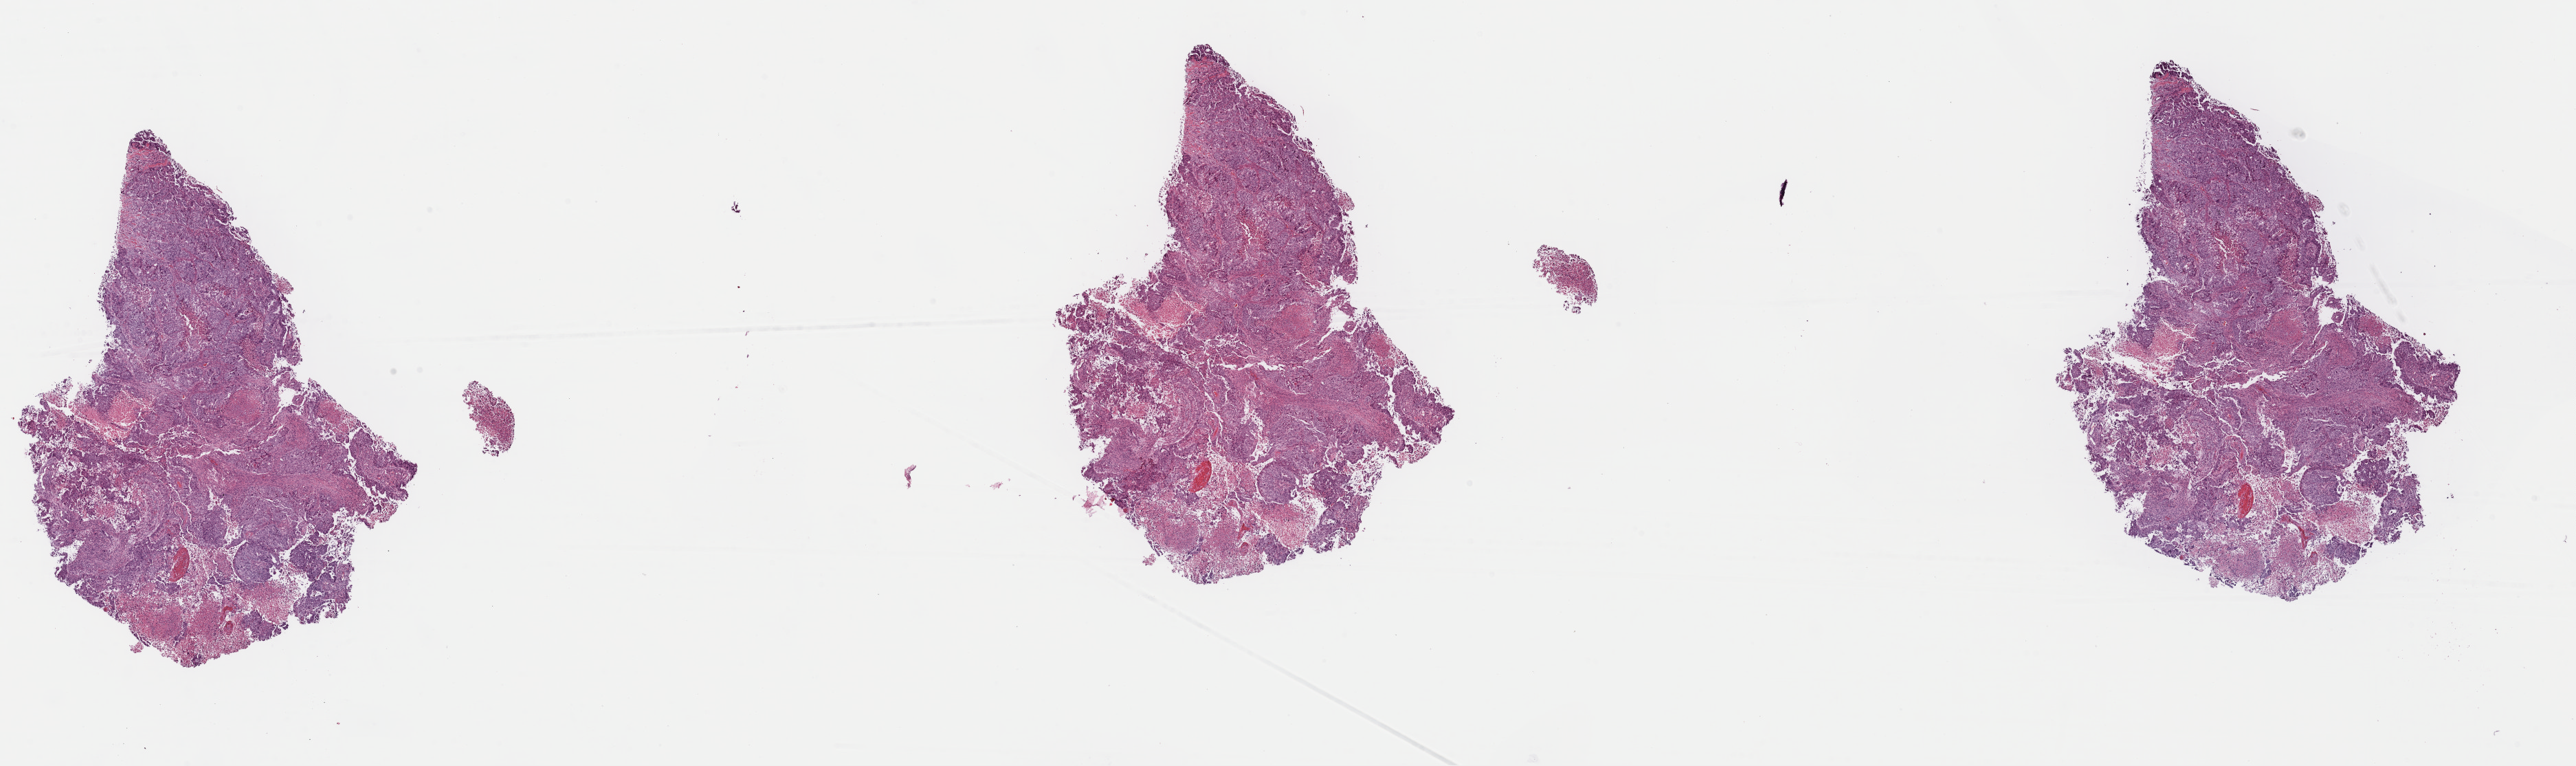
H&E whole-slide image — shown as a low-resolution overview of the whole scanned area (about 29.6 x 8.8 mm, acquisition: 40x scan), formalin-fixed paraffin-embedded (FFPE) diagnostic section, recurrent tumour sample from the uterus. Female, age 74 years at initial diagnosis.
This section: recurrent tumour. Patient diagnosis: Endometrioid adenocarcinoma, NOS (endometrium).